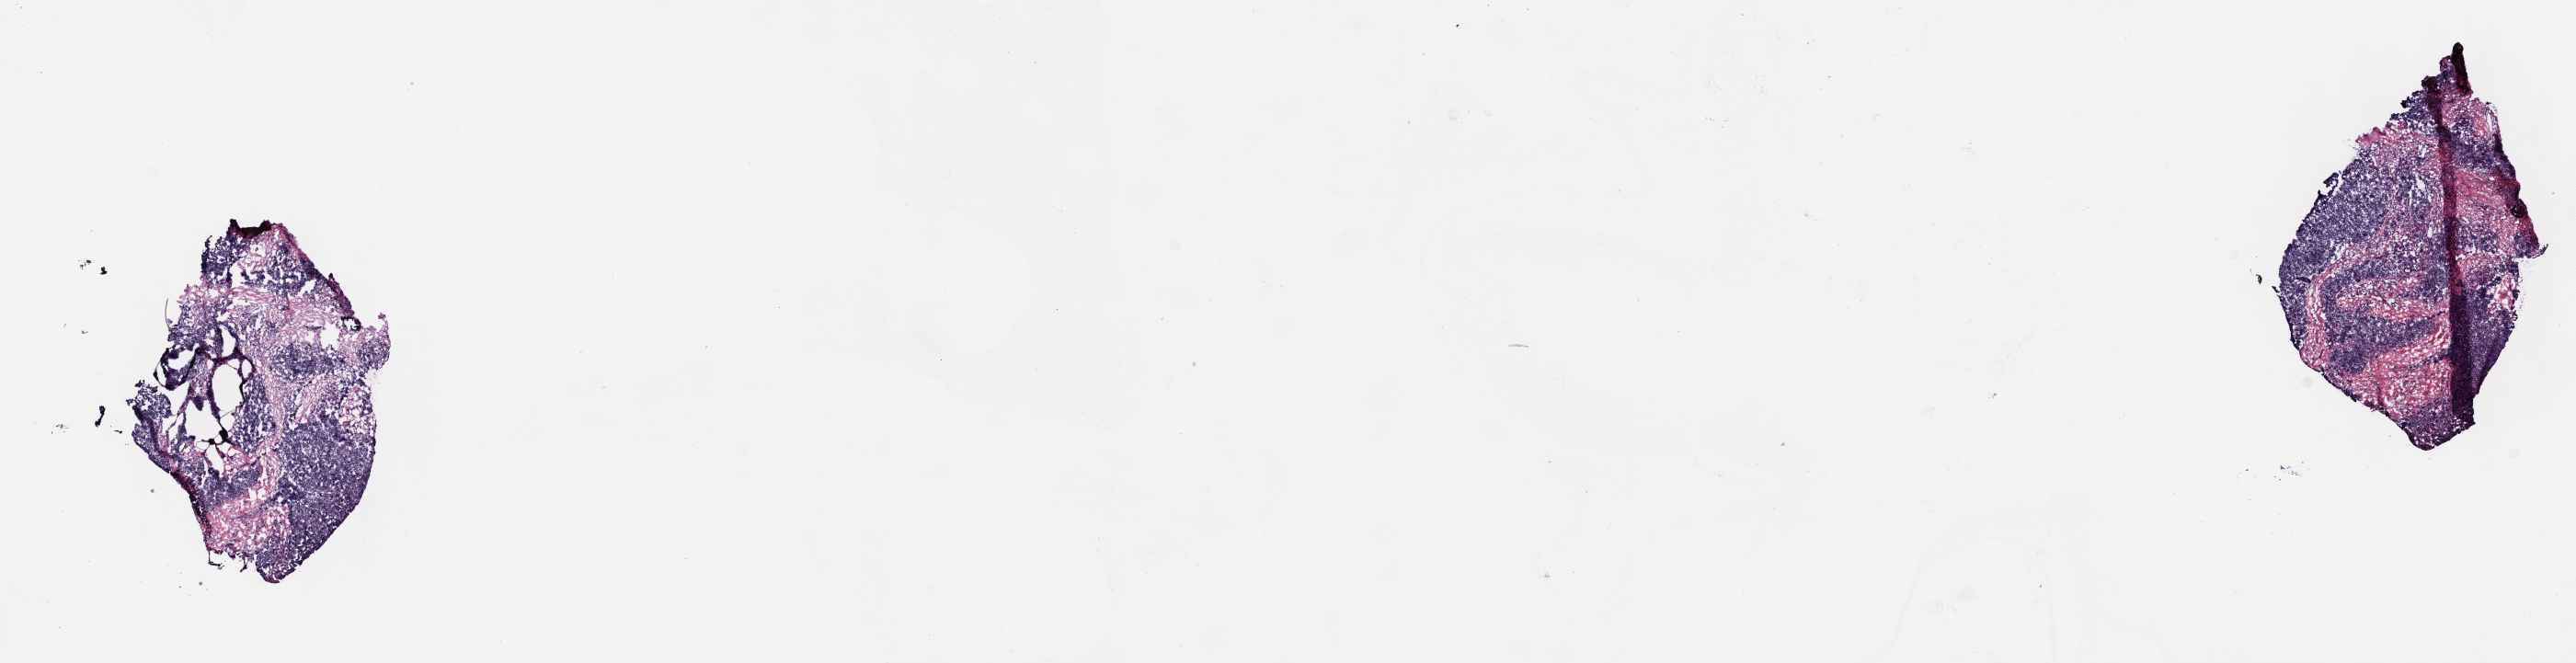
Whole-slide histology image, Hematoxylin and eosin (H&E) stained, shown as a low-resolution overview of the whole scanned area (about 22.7 x 5.8 mm); frozen section from the top of the tissue portion; thymus, primary tumour sample. Male patient; age at initial diagnosis 68 years. Composition of this section per pathologist review: tumour cells 80%, tumour nuclei 80%.
Pathologic diagnosis: Thymoma, type B2, malignant.